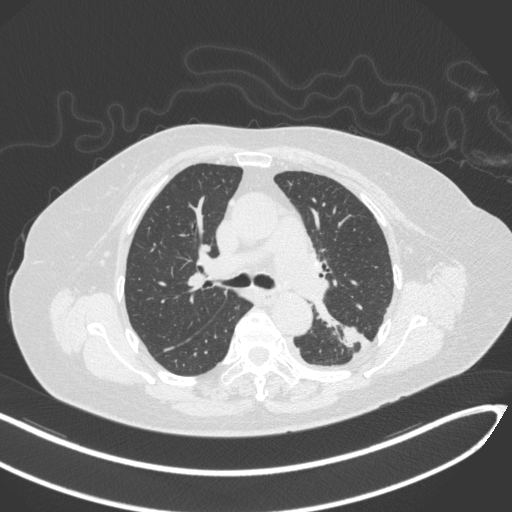
Chest CT, one axial slice; slice 202 of 270 in the series (ordered by position); reconstruction kernel B31f; lung window (W 1500 / L -600 HU); 1 mm slice thickness; 512 × 512 image matrix, field of view 400 × 400 mm. Patient: female, 76 years. Case-level facts recorded for this patient, not image findings: clinical TNM (as recorded): T1c N0 M0.
Structures marked on this image (bounding box drawn by a radiologist):
- lung tumour (recorded histology: adenocarcinoma): bounding box [x1, y1, x2, y2] px = [337, 321, 361, 349]